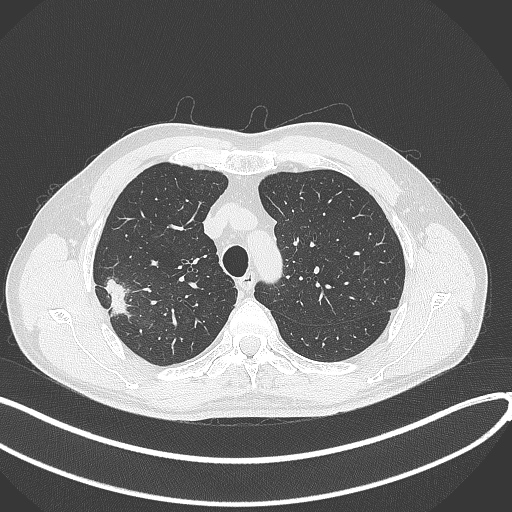
Chest CT, one axial slice; position 323 of 381 along the scan axis; lung window (W 1500 / L -600 HU); 1 mm slice thickness; 512 × 512 image matrix, field of view 400 × 400 mm. Male patient, age 62 years. From the clinical record (not read from this slice): clinical TNM (as recorded): T1c N0 M0; histopathological grade: G2-3.
Outlined on this slice (bounding box drawn by a radiologist):
- lung tumour (recorded histology: adenocarcinoma): bounding box [x1, y1, x2, y2] px = [104, 274, 131, 319]